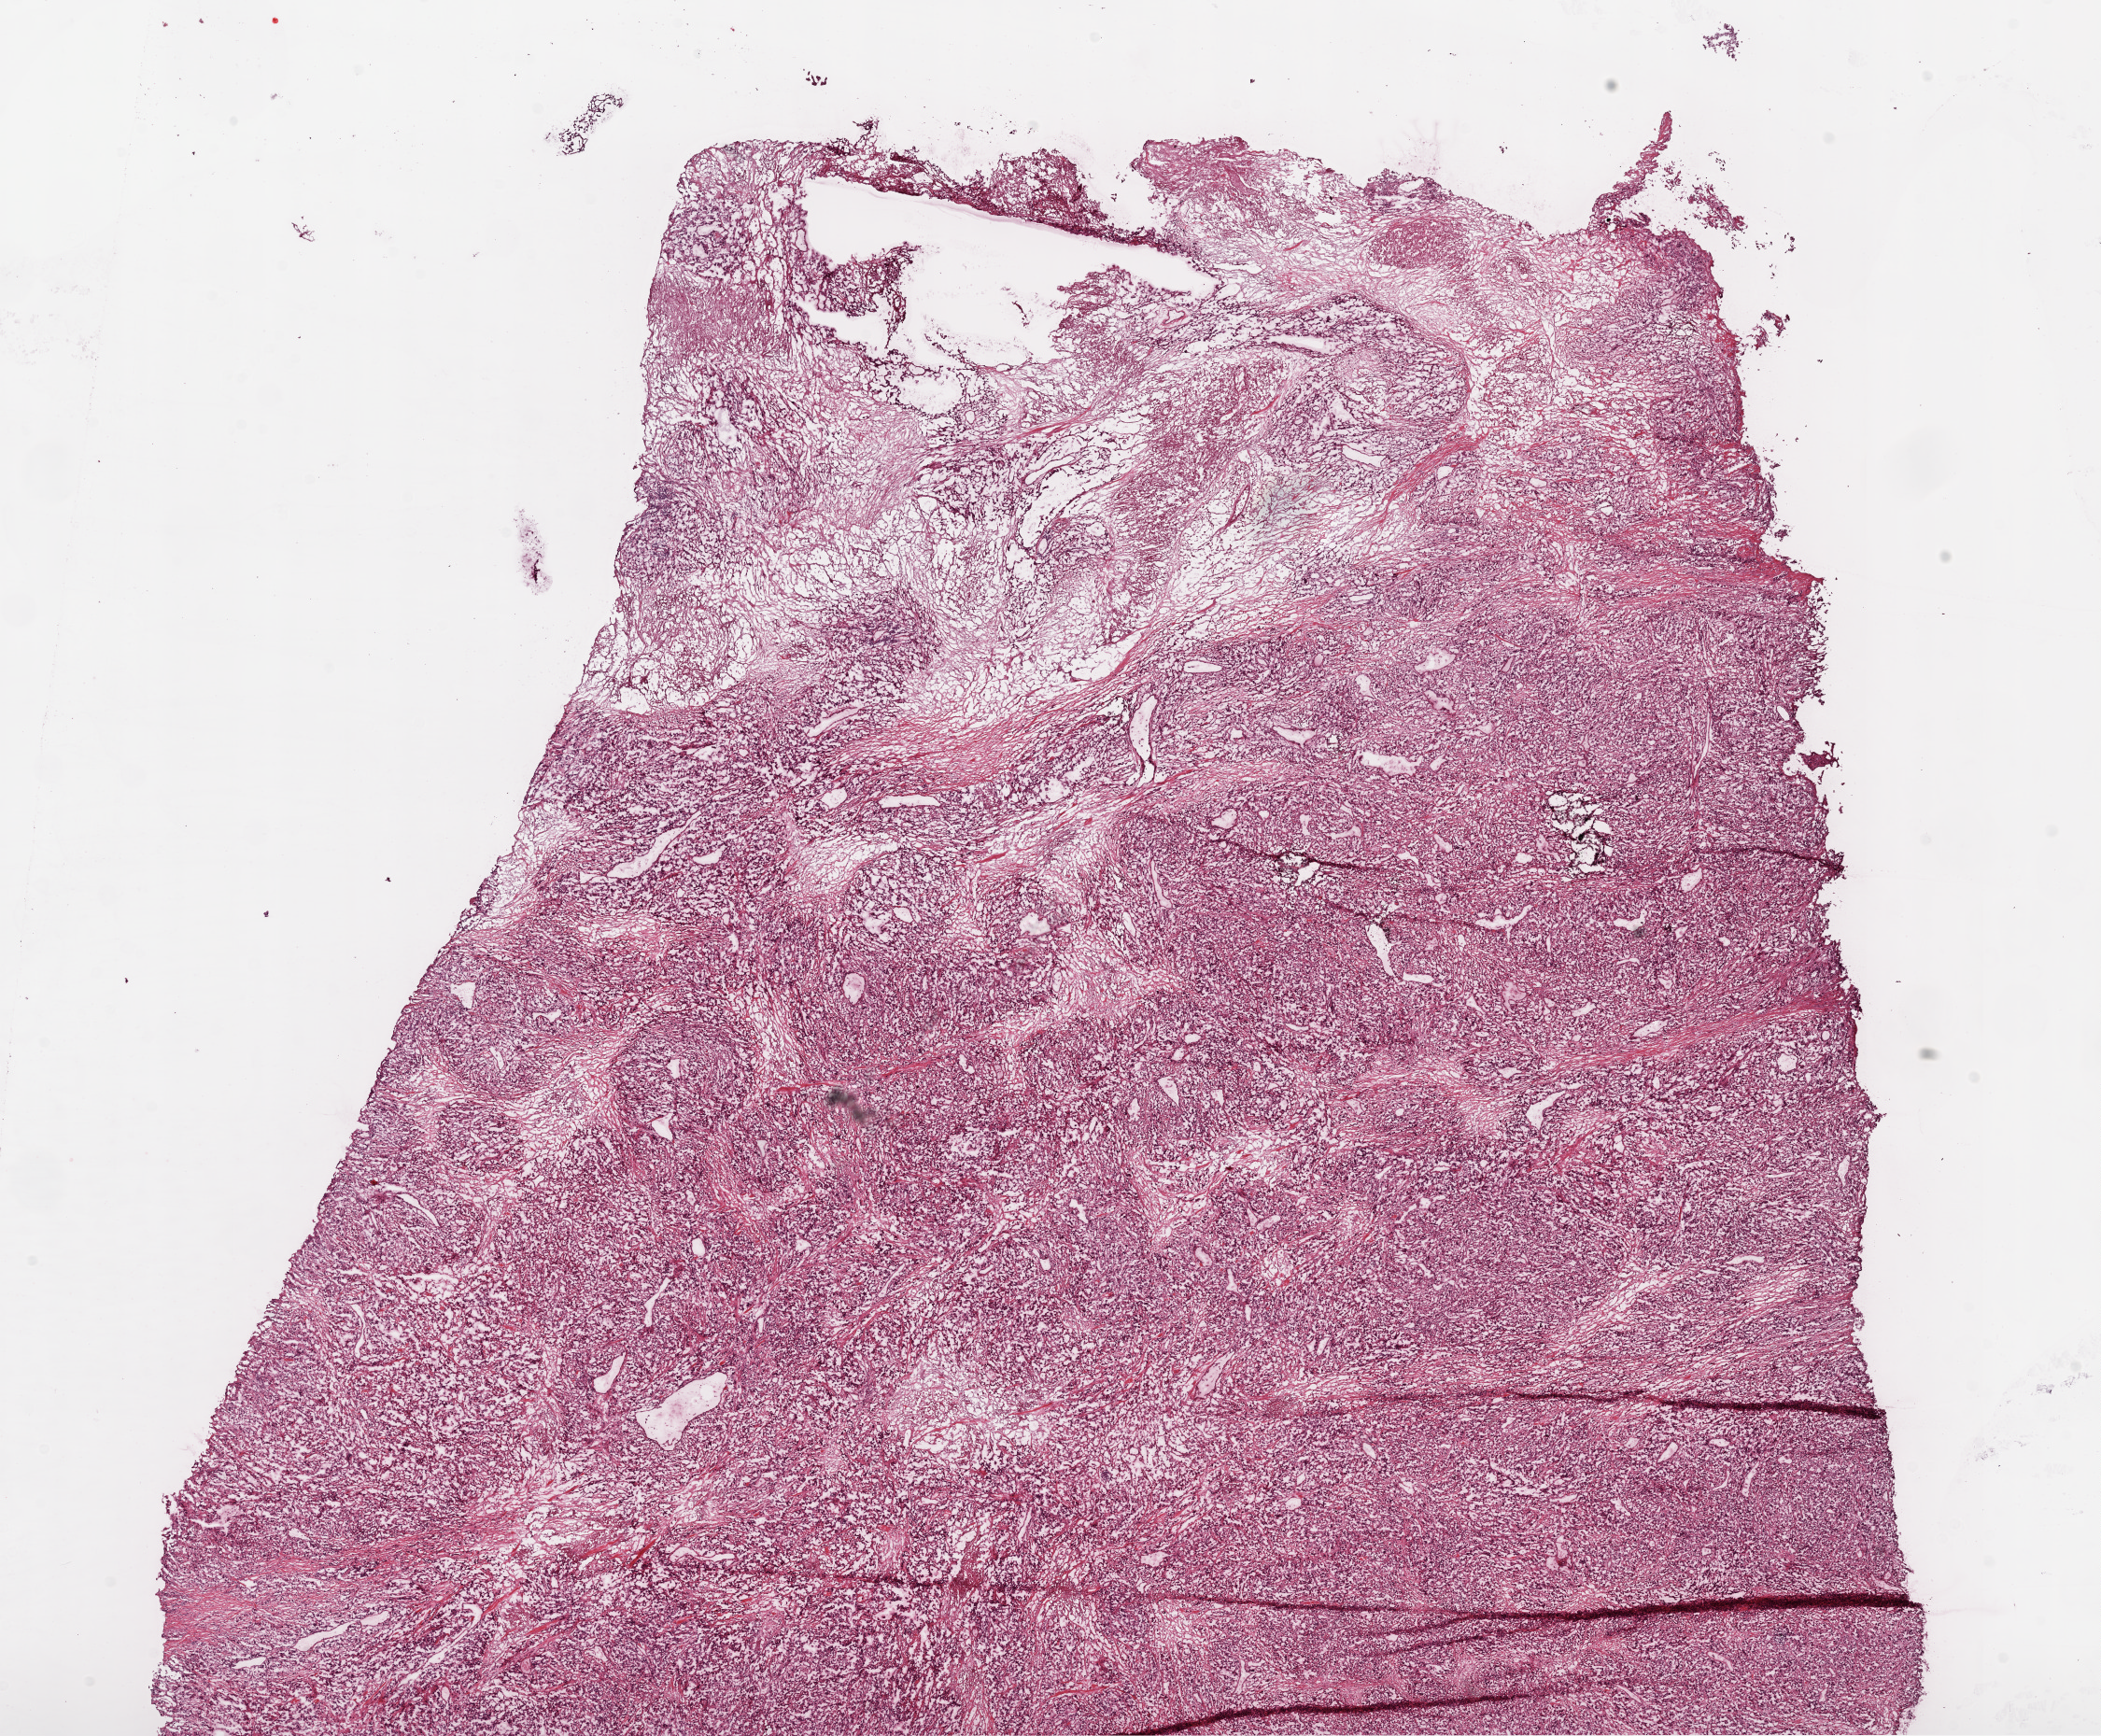
Digitized H&E-stained tissue section (whole slide), low-resolution overview of the scanned area, about 18.1 x 14.9 mm (slide scanned at 20x), frozen section, kidney, primary tumour sample. Patient: female, age at initial diagnosis 74 years. Histologic grade: G4 (undifferentiated). Pathologist review of this section (percent, as recorded): tumour cells 85%, tumour nuclei 80%, normal cells 0%, stromal cells 15%, necrosis 0%.
Lymph nodes positive (case pathology): 0 of 10 examined. AJCC pathologic stage: IV. Pathologic diagnosis: Clear cell adenocarcinoma, NOS.